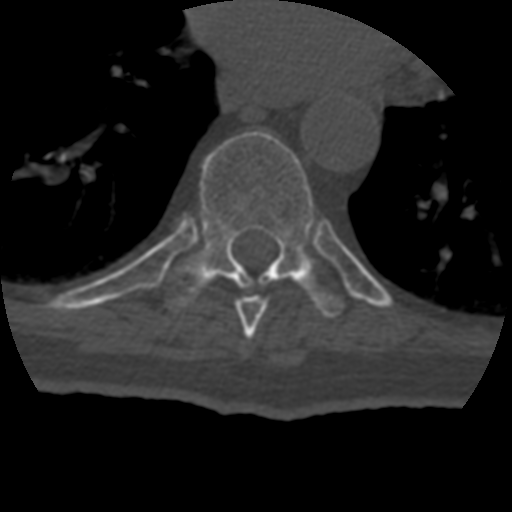
CT including the spine, one axial slice. Position 247 of 399 along the scan axis. Reconstruction kernel STANDARD. 120 kVp. Bone window (W 1800 / L 400 HU). 512 × 512 image matrix, field of view 160 × 160 mm. Patient age 69 years. From the clinical record (not read from this slice): primary cancer: prostate.
Outlined on this slice (semi-automatically segmented with operator editing):
- T8 vertebra: box from (x=236, y=296) to (x=267, y=338) px
- T9 vertebra: (x=166, y=131)–(x=345, y=318)